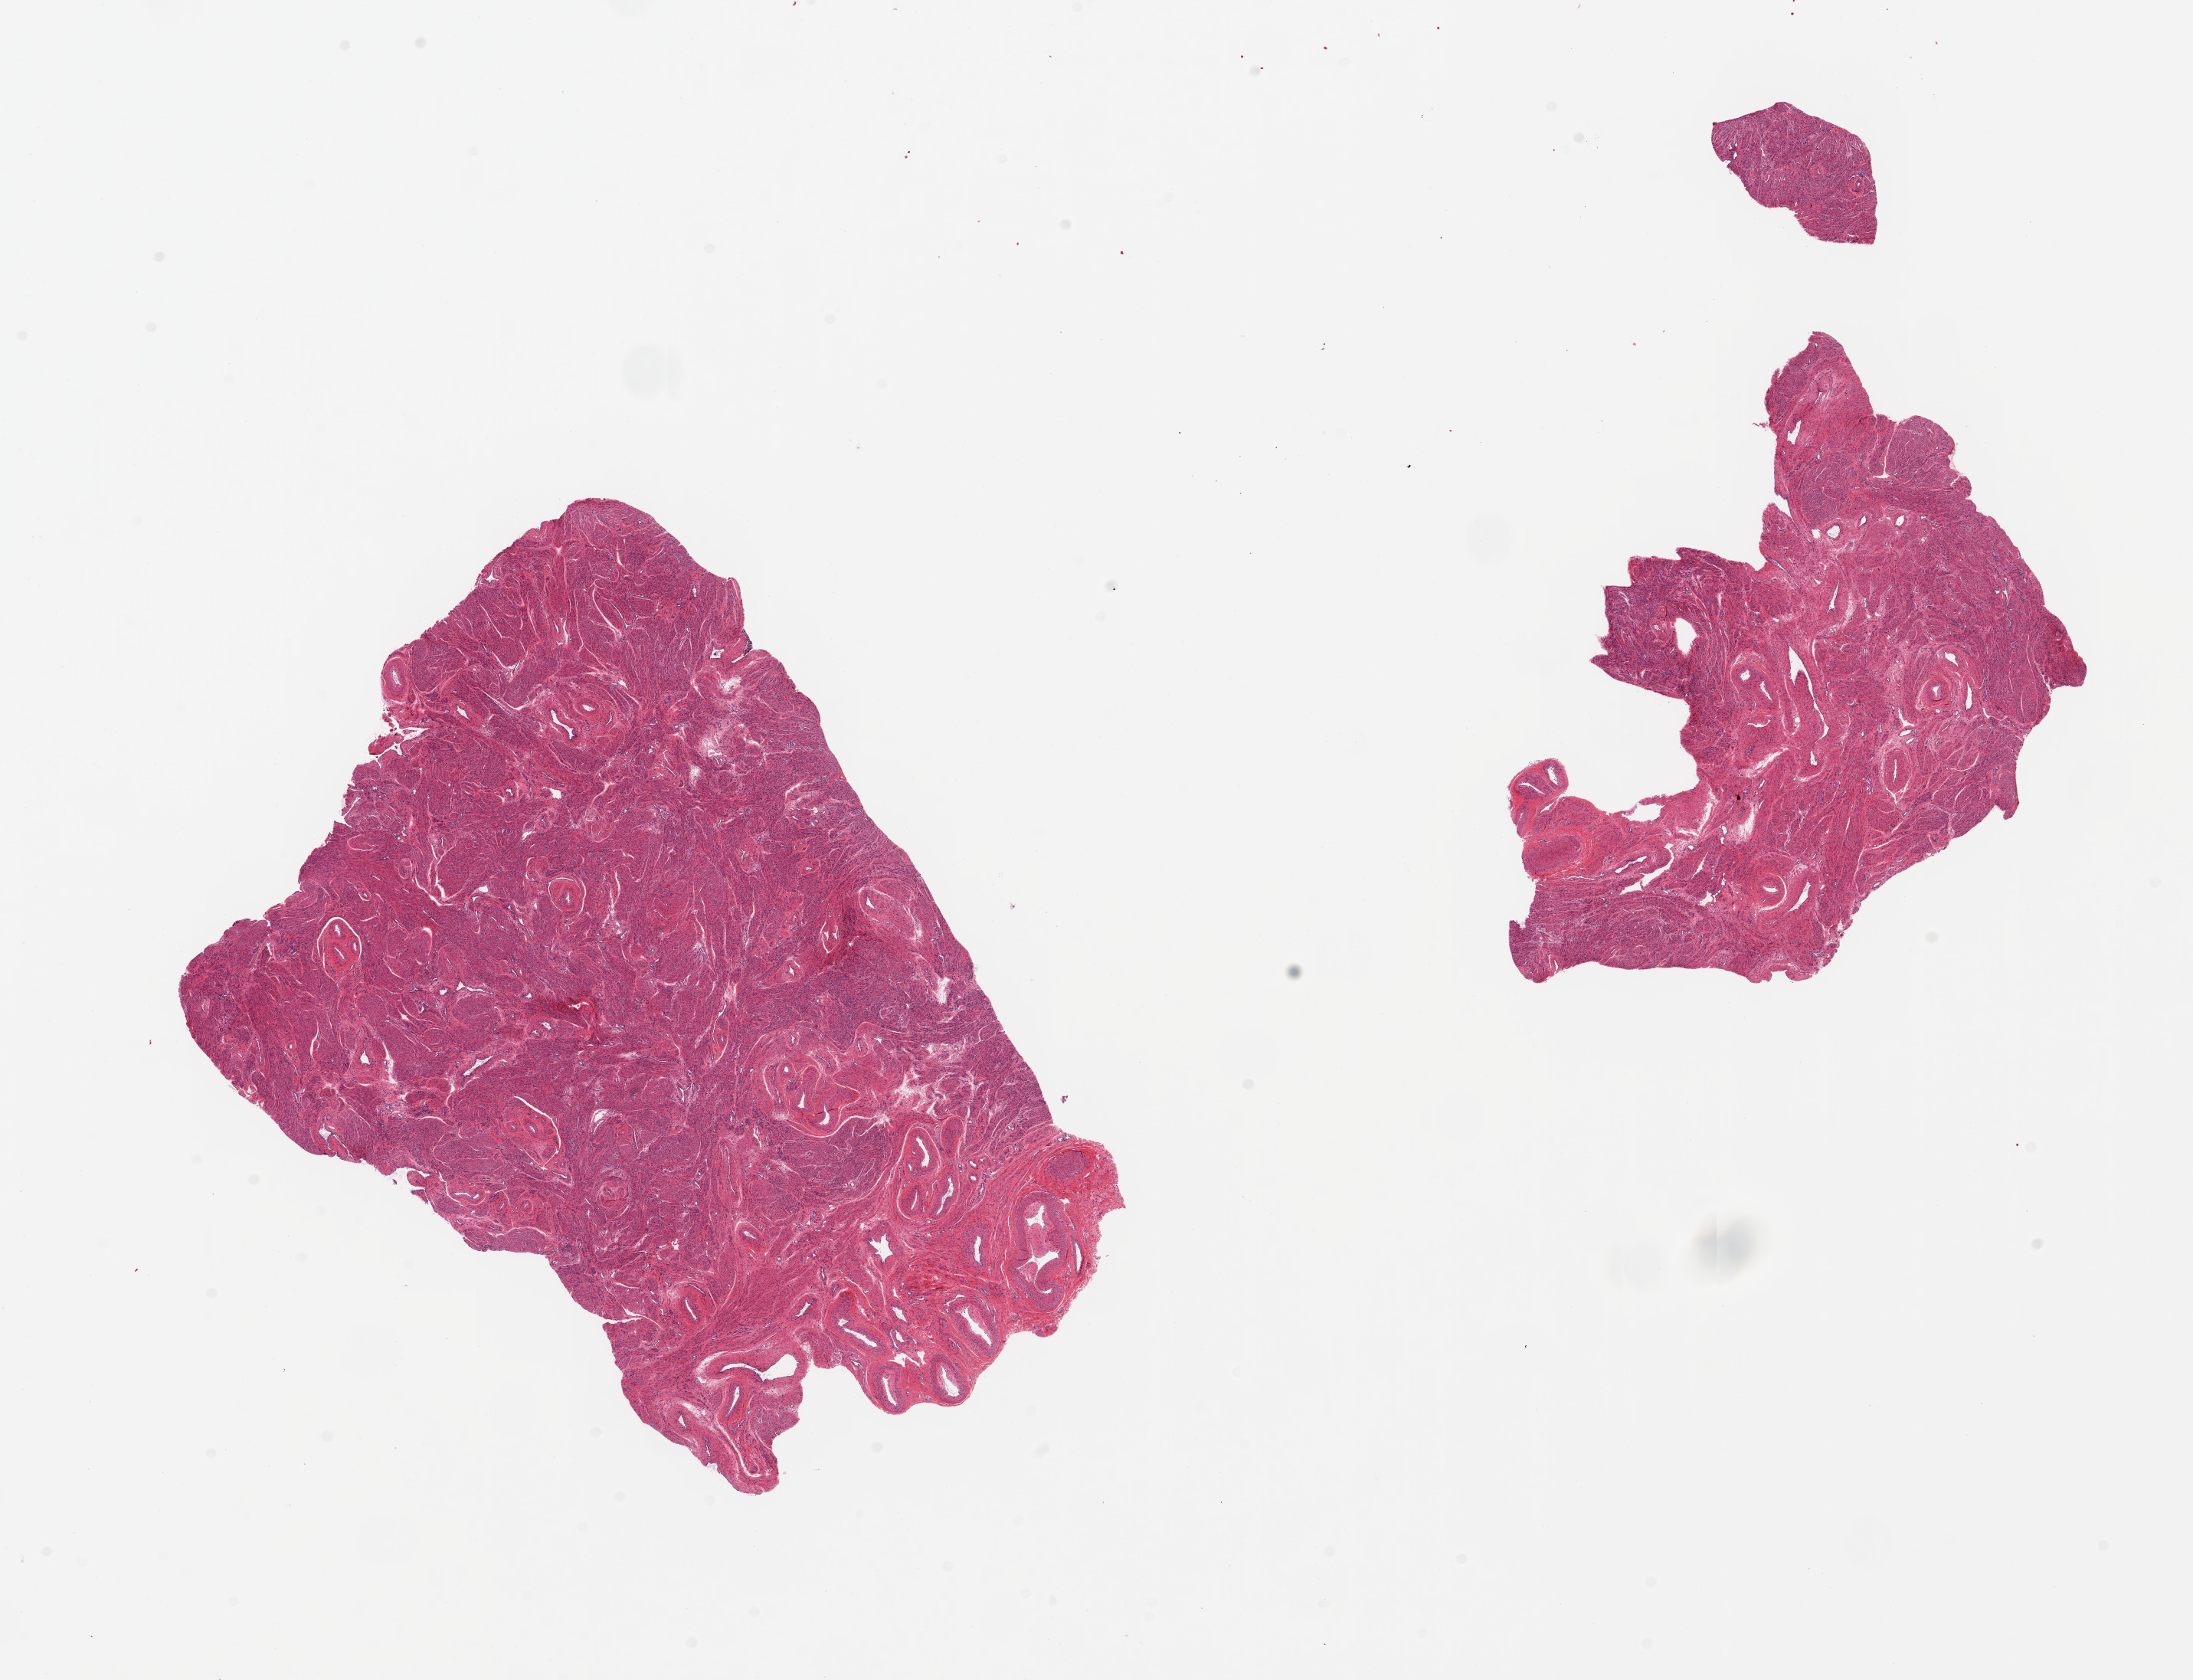
Whole-slide image, haematoxylin and eosin stain, low-resolution overview of the scanned area, about 22.6 x 17.3 mm. PAXgene-fixed, paraffin-embedded tissue. Section of uterus (target tissue). Donor tissue sample.
Reviewer comment on this tissue sample: 2 pieces; myometrium only (in these cuts).